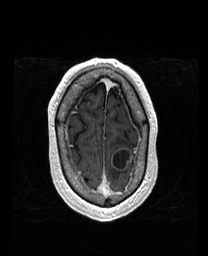
Brain MRI from a brain-tumour surgery series, one axial slice; slice 150 of 192 in the series (ordered by position); T1-weighted post-contrast; 1 mm slice thickness; 208 × 256 image matrix, field of view 211 × 260 mm. From the clinical record (not read from this slice): histopathology: Metastatic Carcinoma from Lung Adenocarcinoma; tumour location: Left Frontal.
Annotated regions visible in this slice (manually delineated by an expert):
- tumour: box from (x=113, y=147) to (x=132, y=170) px